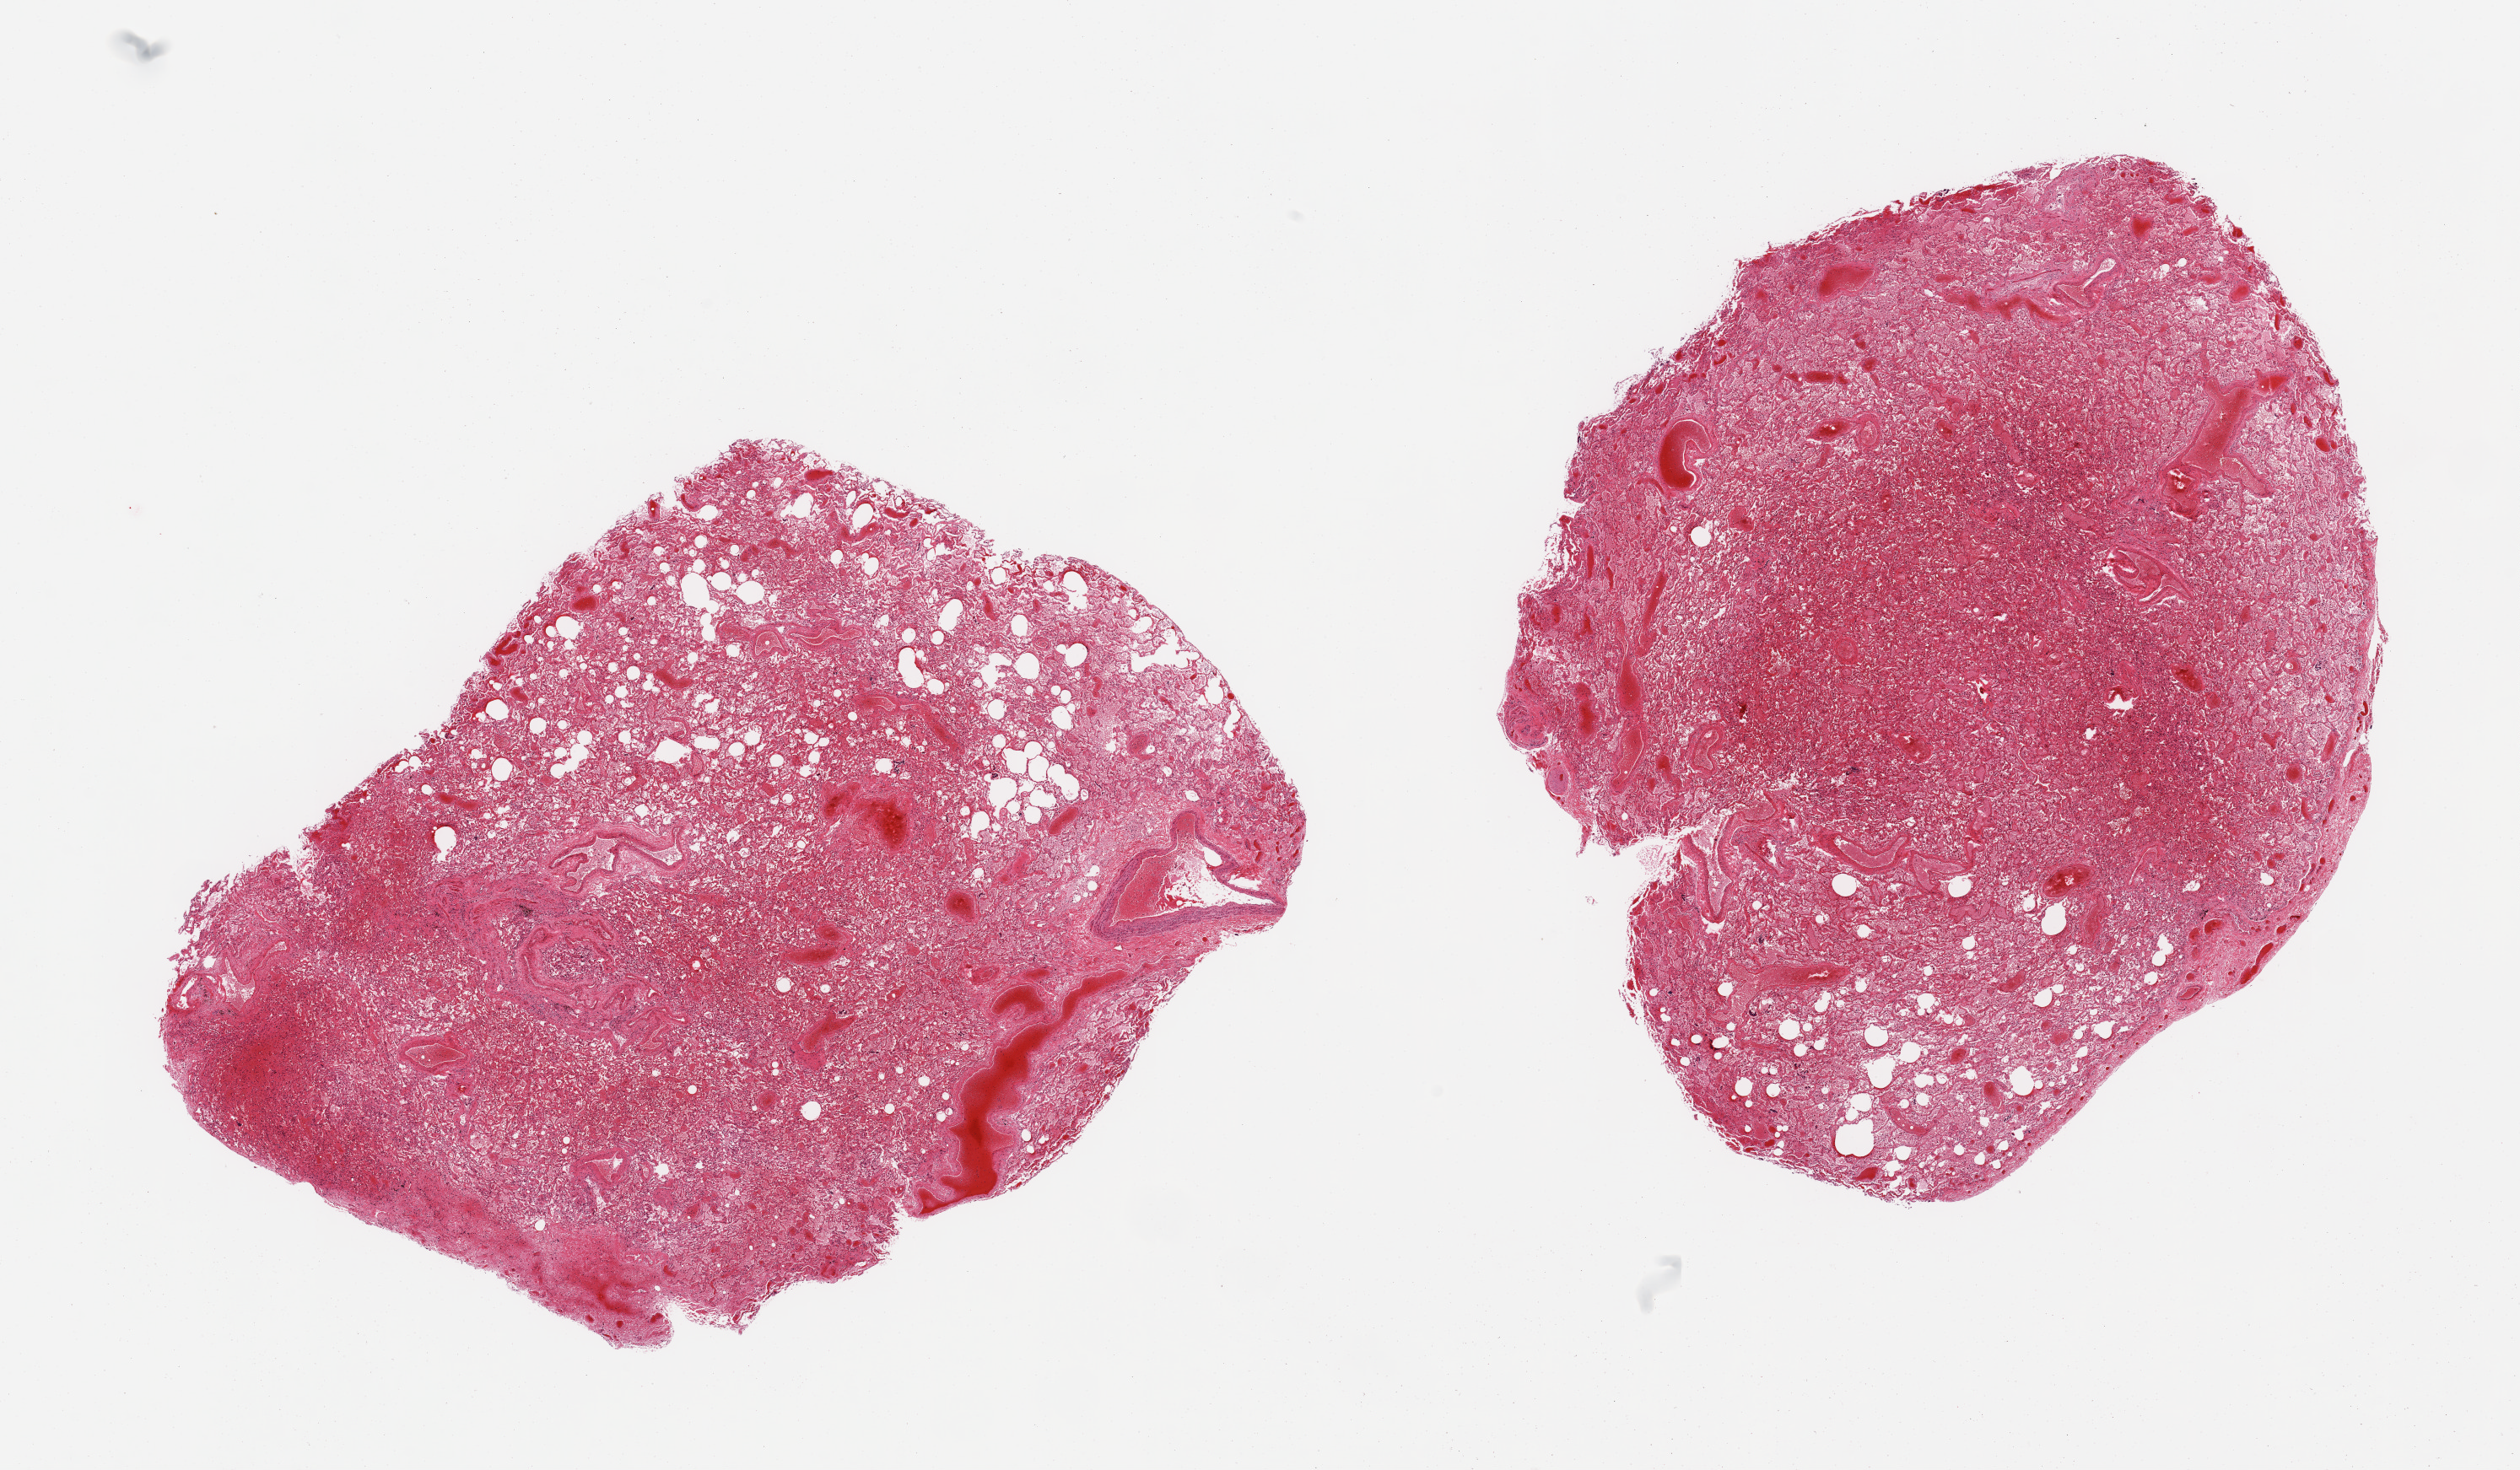
Whole-slide image, H&E stain, low-resolution overview of the scanned area, about 23.6 x 13.8 mm, PAXgene-fixed, paraffin-embedded tissue, target tissue: lung, tissue donor sample. Donor: male.
Review note (as recorded): 2 pieces, marked edema and congestion, evidence of chronicity.